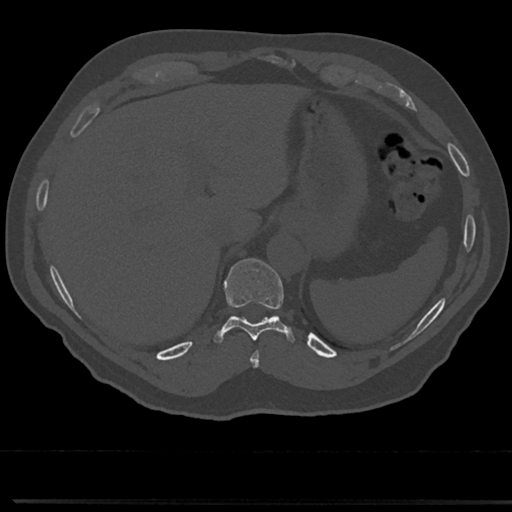
CT including the spine, one axial slice; slice 254 of 817 in the series (ordered by position); reconstruction kernel Br40s/3; 120 kVp; bone window (W 1800 / L 400 HU); 0.5 mm slice thickness; 512 × 512 image matrix, field of view 355 × 355 mm. Patient: male, 61 years. From the clinical record (not read from this slice): primary cancer: prostate.
Annotated regions visible in this slice (semi-automatic segmentation, software-assisted and operator-edited):
- T10 vertebra: bounding box [x1, y1, x2, y2] px = [209, 259, 299, 345]
- T9 vertebra: [251, 342, 260, 368]